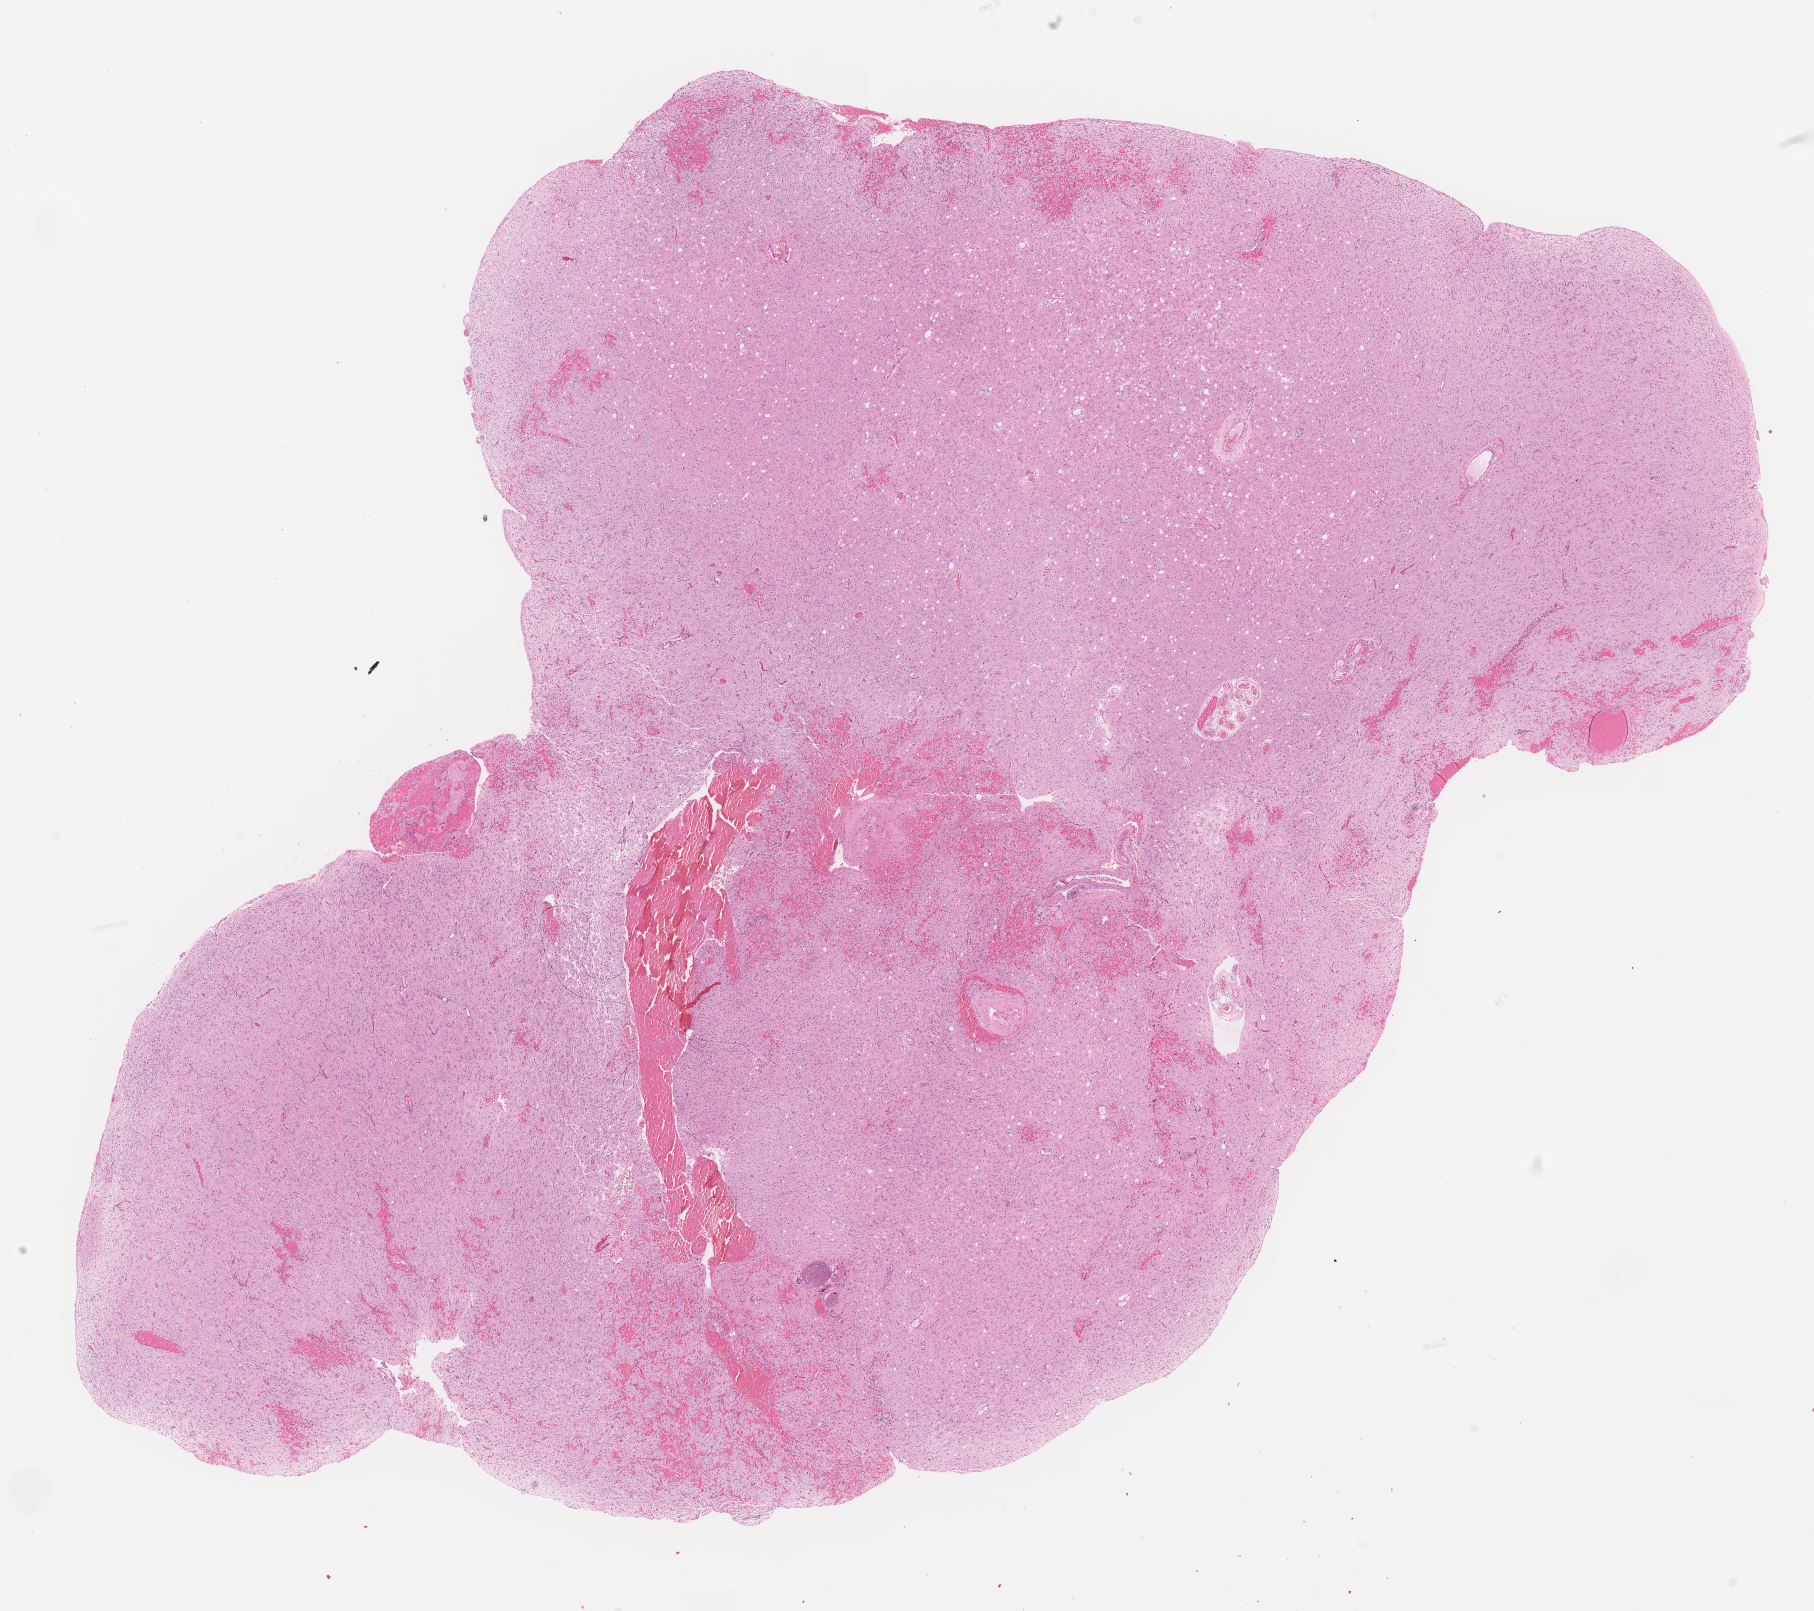
H&E-stained whole-slide image — a low-resolution overview of the entire scanned area, about 14.6 x 13.0 mm; FFPE section; primary tumour sample from the brain. Male, age 52 years at initial diagnosis. Histologic grade: G3 (poorly differentiated).
Pathologic diagnosis: Oligodendroglioma, anaplastic (cerebrum).